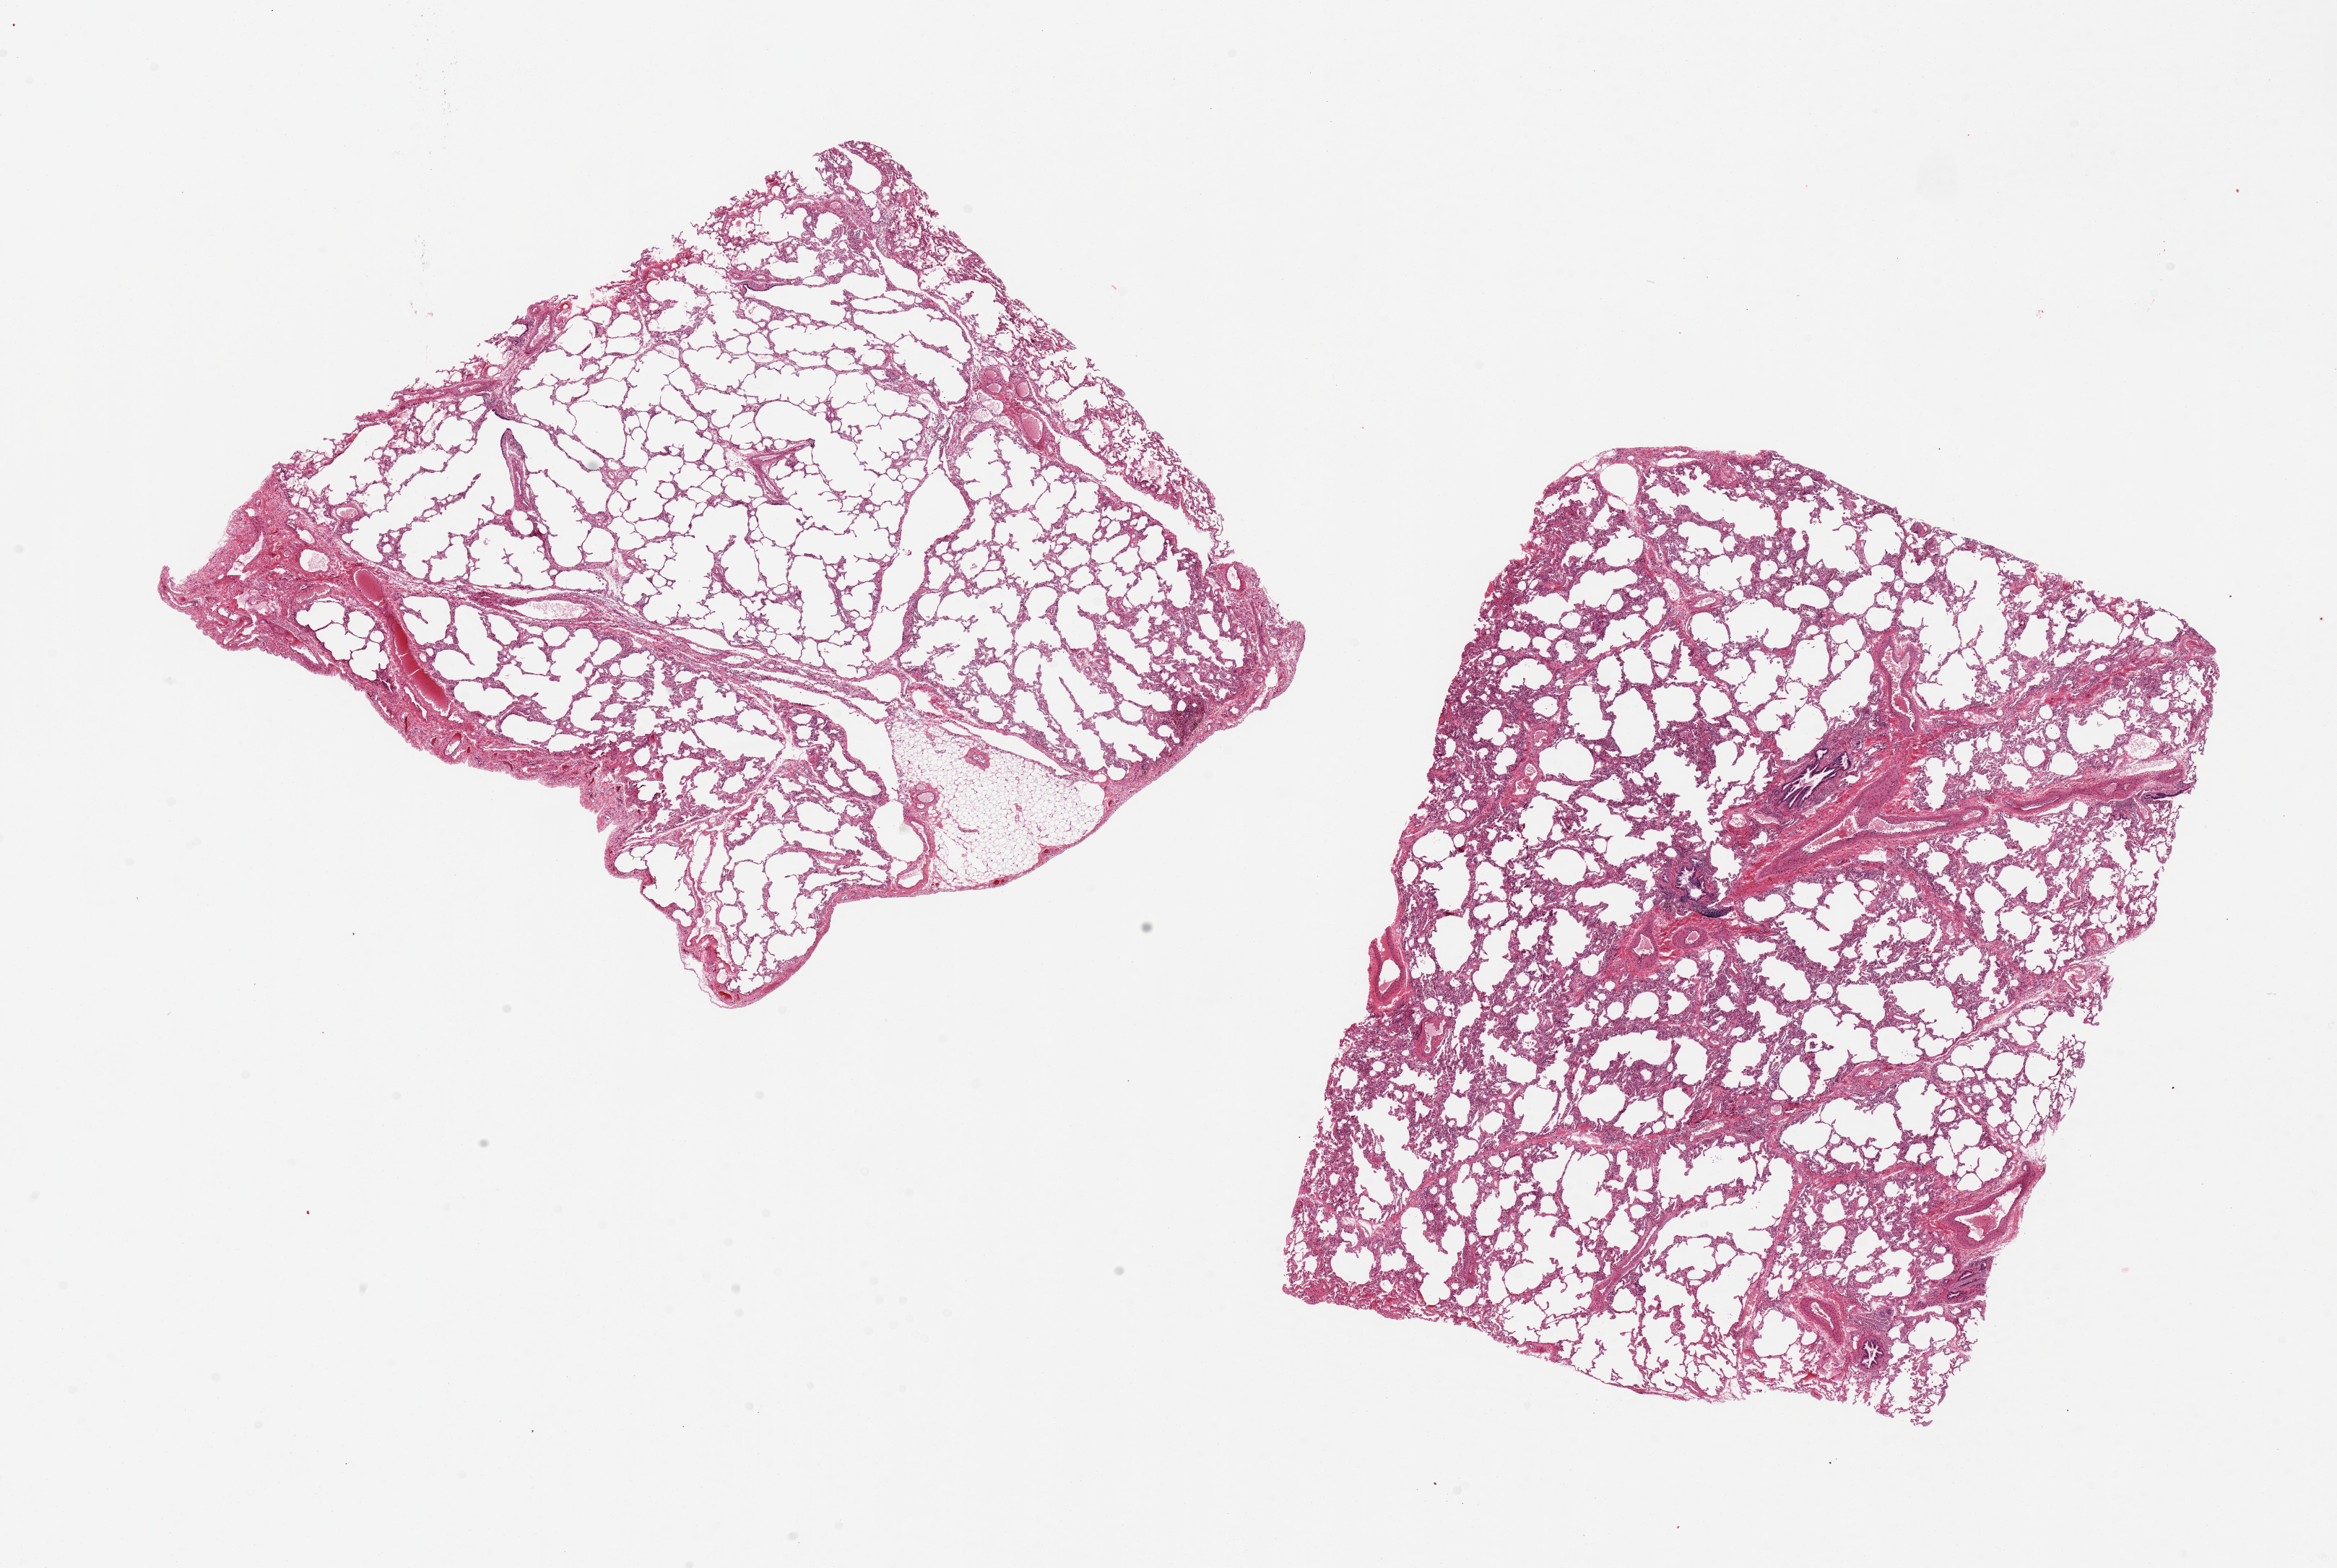
Digitized hematoxylin and eosin (H&E)-stained section — shown as a low-resolution overview of the whole scanned area (about 25.6 x 17.2 mm), PAXgene-fixed, paraffin-embedded tissue, section of lung (target tissue), tissue donor sample. Female donor.
Pathologist's review note for this sample: 2 pieces 10x8 & 9x8 mm; panacinar emphysema; 2x1.6 mm pleural adipose focus (pleural tissue should be avoided).